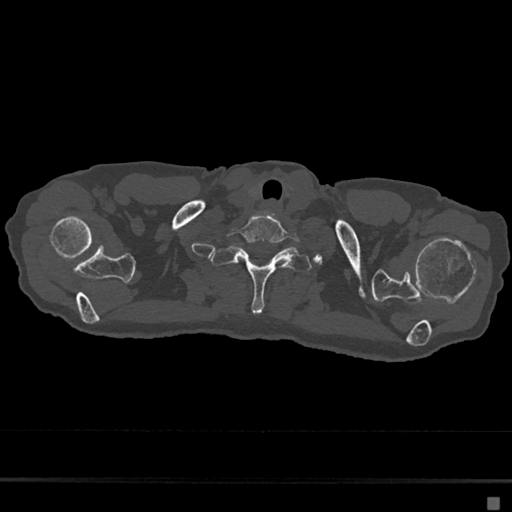
CT including the spine, one axial slice. Reconstruction kernel Br40s/3. Bone window (W 1800 / L 400 HU). 0.5 mm slice thickness. 512 × 512 image matrix, field of view 360 × 360 mm. Patient: female, 68 years. From the clinical record (not read from this slice): primary cancer: renal.
Outlined on this slice (semi-automatically segmented with operator editing):
- T1 vertebra: box from (x=211, y=247) to (x=312, y=313) px